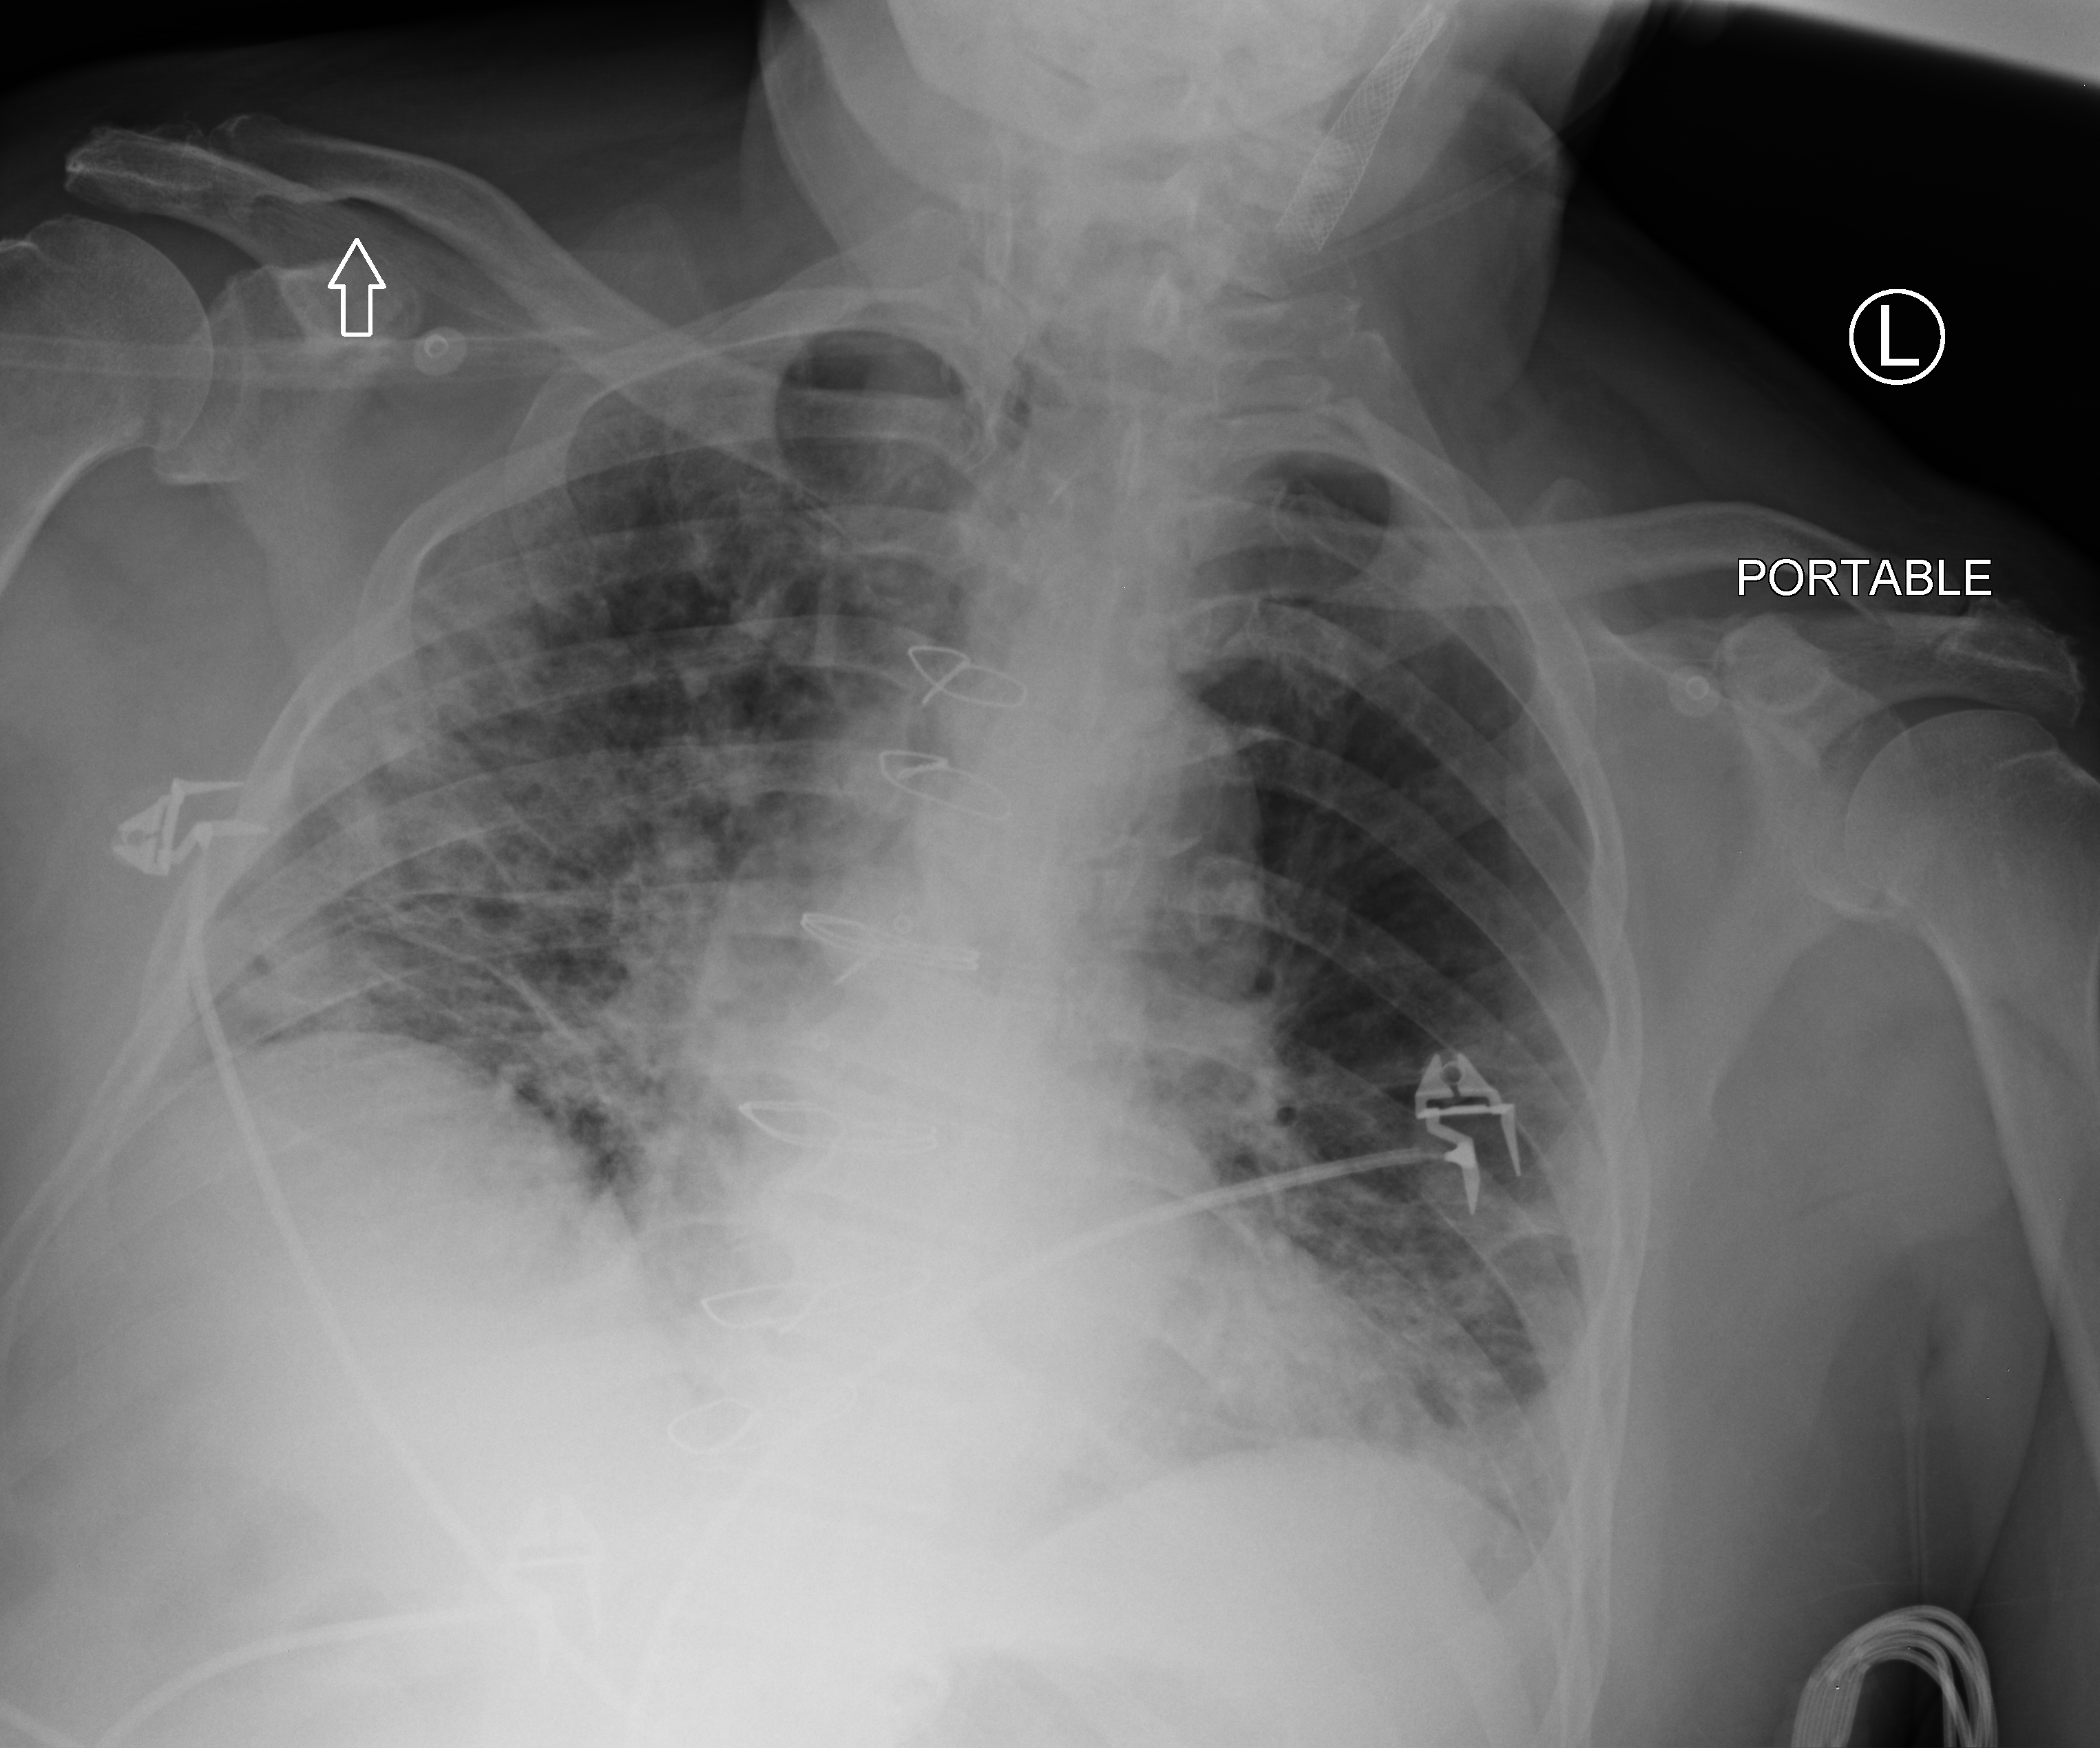
Portable chest radiograph; anteroposterior (AP) projection. Patient hospitalised with COVID-19; male, aged 75–90 years.
From the hospital-stay record, not from the radiograph (when in the stay this image was taken is not recorded): chronic kidney disease (admission record): no.